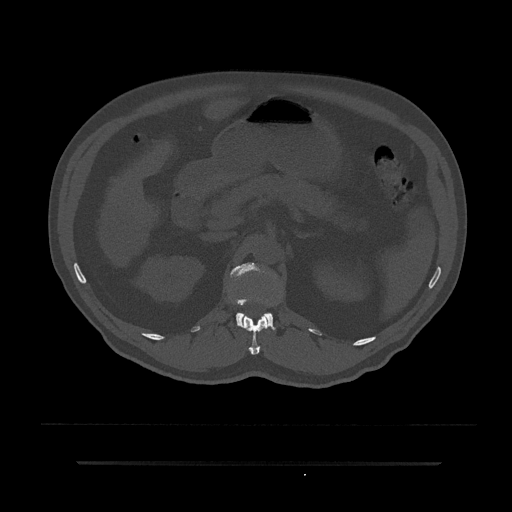
CT including the spine, one axial slice; slice 179 of 797 in the series (ordered by position); 120 kVp; bone window (W 1800 / L 400 HU); 0.5 mm slice thickness; 512 × 512 image matrix. Patient: male, 59 years. Case-level facts recorded for this patient, not image findings: primary cancer: bile ducts; vertebrae with lytic lesions (as recorded): T10.
Outlined on this slice (semi-automatically segmented with operator editing):
- L1 vertebra: bounding box [x1, y1, x2, y2] px = [230, 263, 275, 329]
- T12 vertebra: [241, 314, 269, 355]